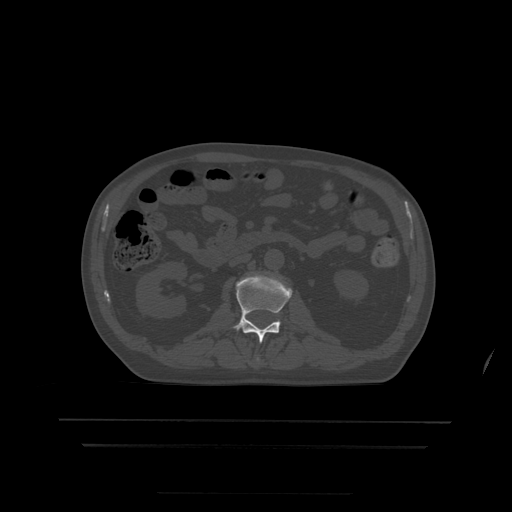
CT including the spine, one axial slice; position 143 of 522 along the scan axis; bone window (W 1800 / L 400 HU); 1.25 mm slice thickness; 512 × 512 image matrix. Patient age 68 years. From the clinical record (not read from this slice): primary cancer: urothelial.
Outlined on this slice (semi-automatically segmented with operator editing):
- L1 vertebra: box from (x=257, y=358) to (x=259, y=361) px
- L2 vertebra: (x=233, y=275)–(x=293, y=343)